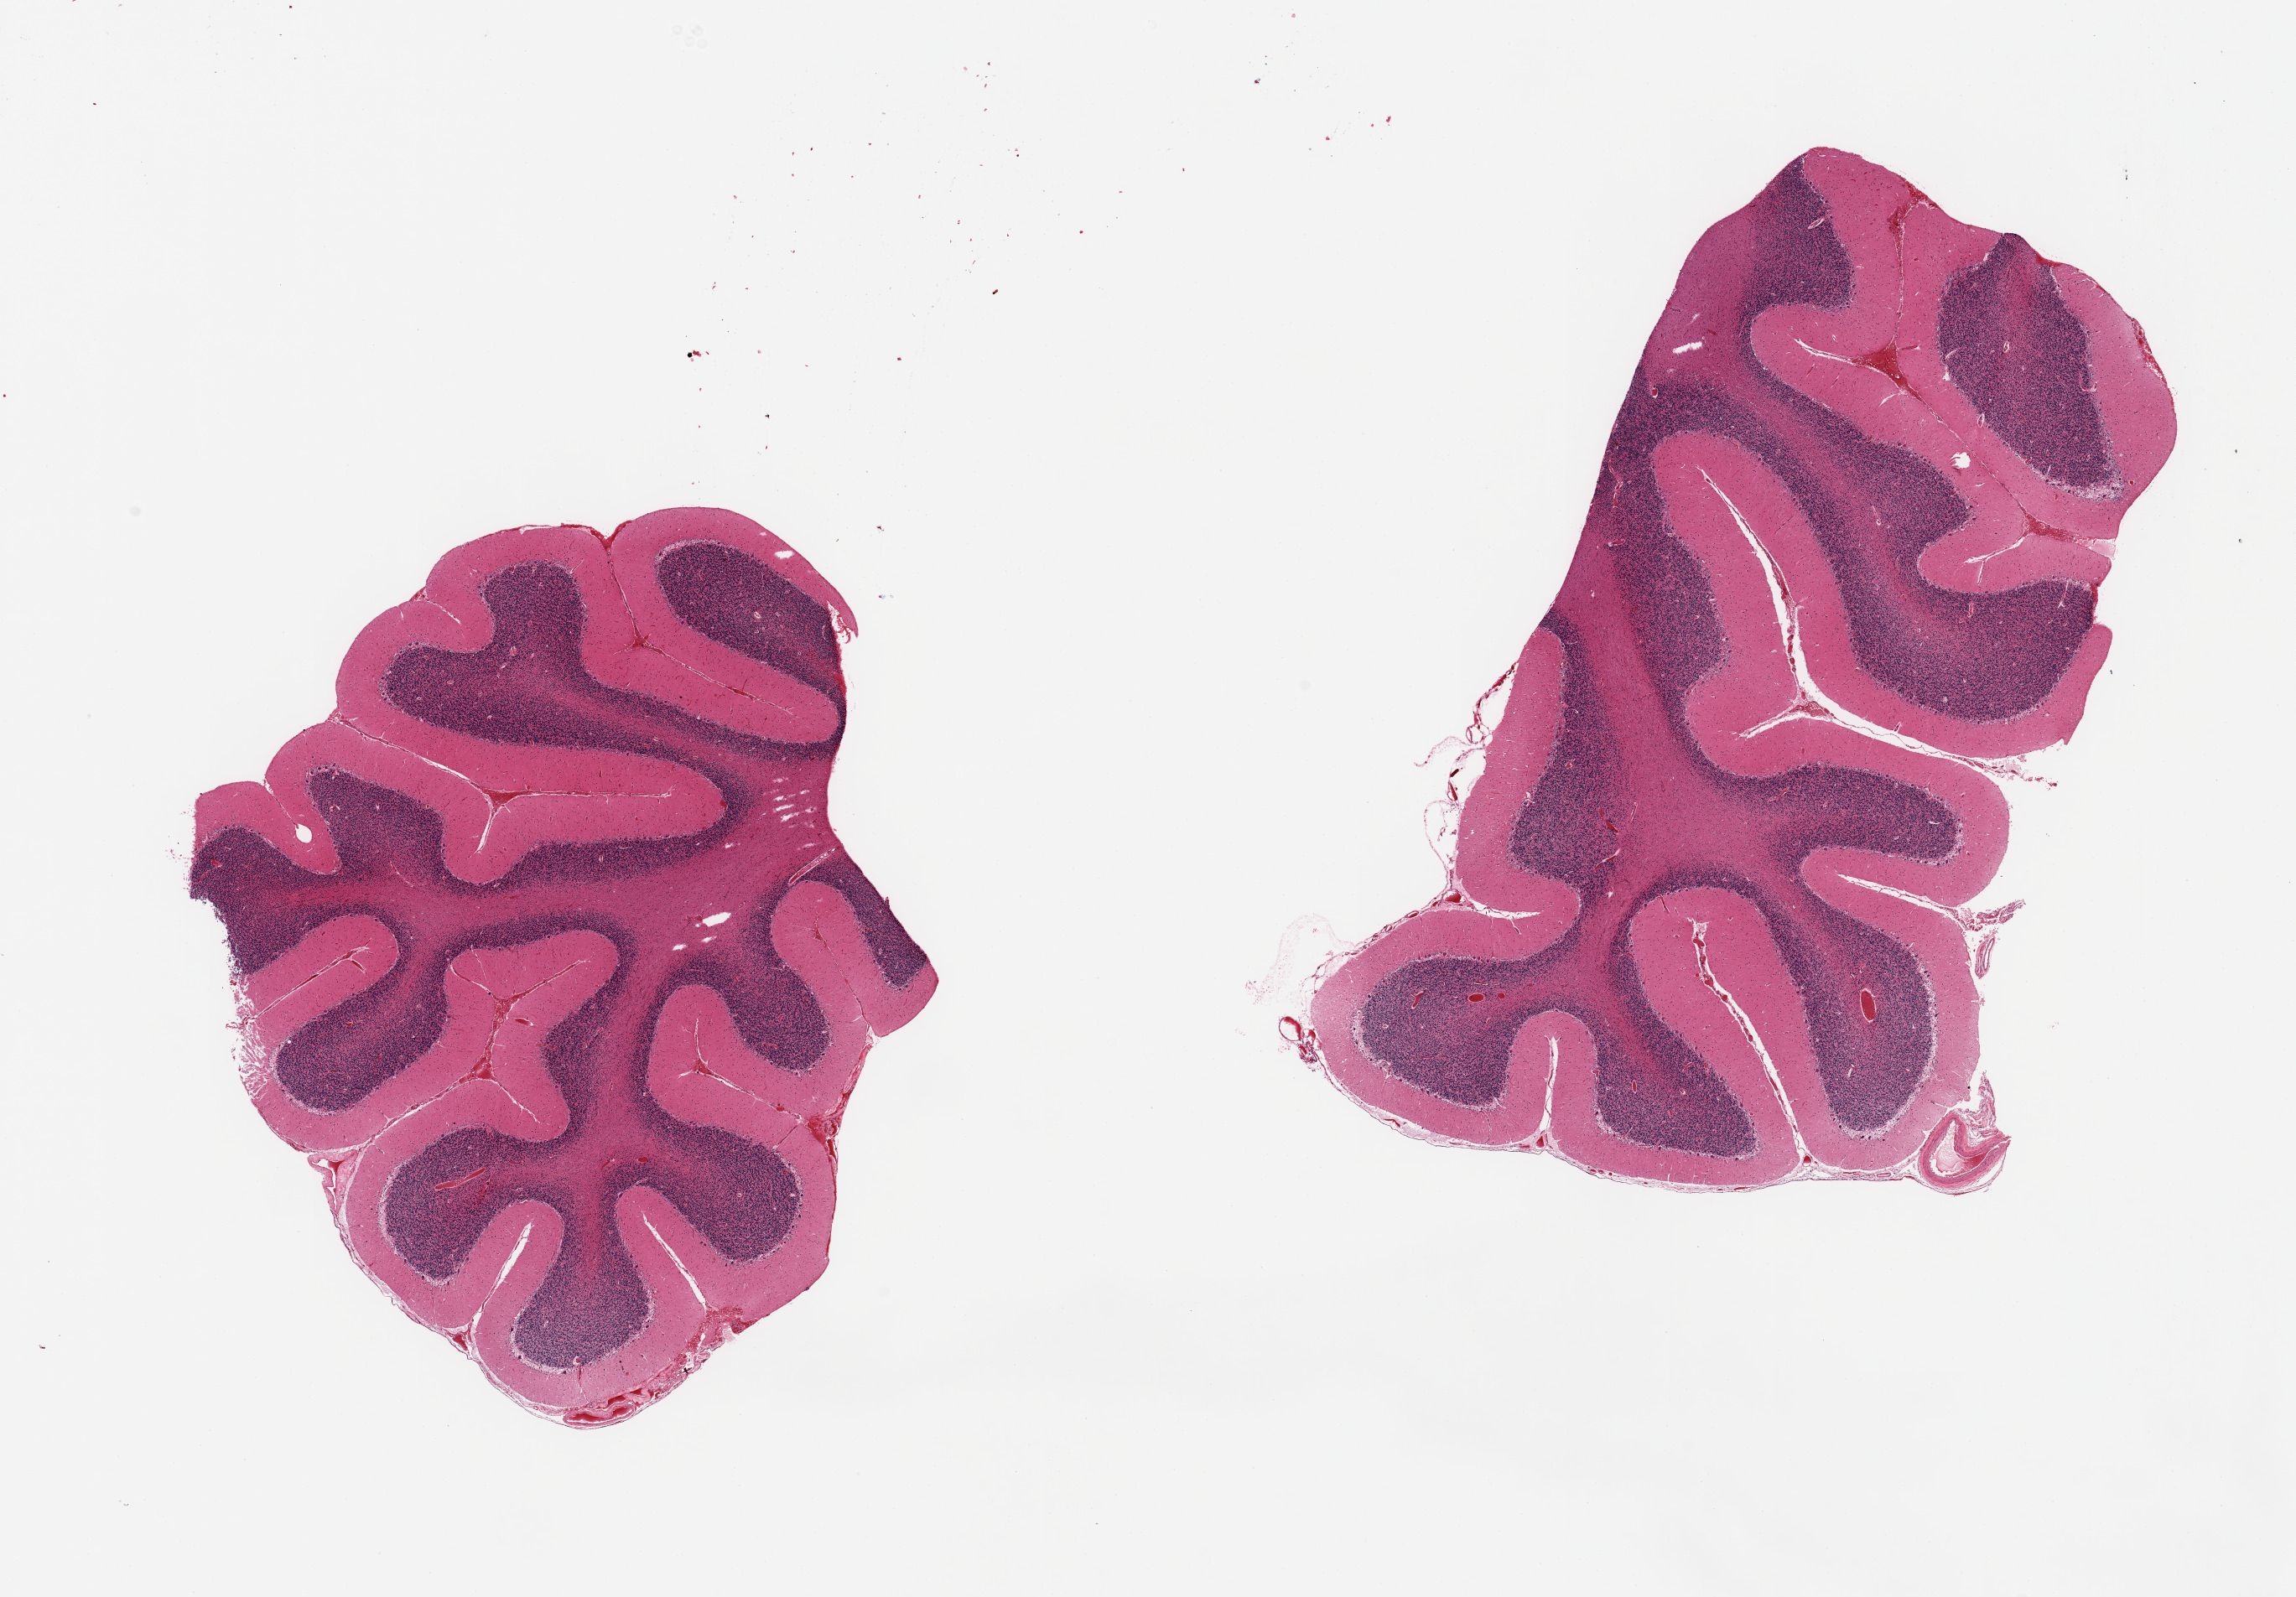
Whole-slide image, haematoxylin and eosin stain, brightfield, shown as a low-resolution overview of the whole scanned area (about 21.7 x 15.1 mm, acquisition: 20x scan), PAXgene-fixed, paraffin-embedded tissue, section of cerebellum (target tissue), tissue donor sample. Male donor.
Pathologist's review note for this sample: 2 pieces, no abnormalities.